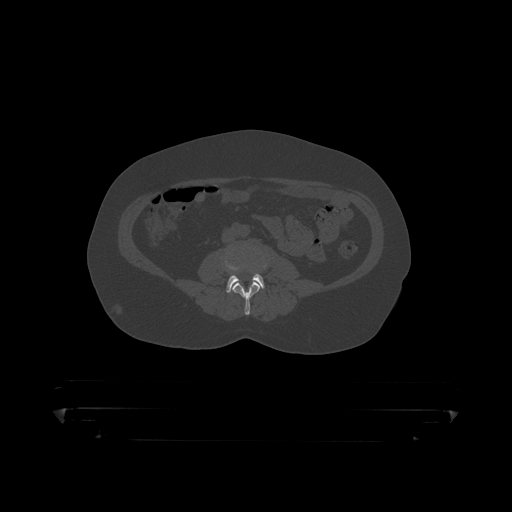
CT including the spine, one axial slice; slice 78 of 390 in the series (ordered by position); bone window (W 1800 / L 400 HU); 1.25 mm slice thickness; 512 × 512 image matrix, field of view 650 × 650 mm. Patient: male, 60 years. From the clinical record (not read from this slice): primary cancer: prostate.
Outlined on this slice (semi-automatically segmented with operator editing):
- L3 vertebra: bounding box [x1, y1, x2, y2] px = [231, 259, 268, 316]
- L4 vertebra: [226, 269, 265, 293]